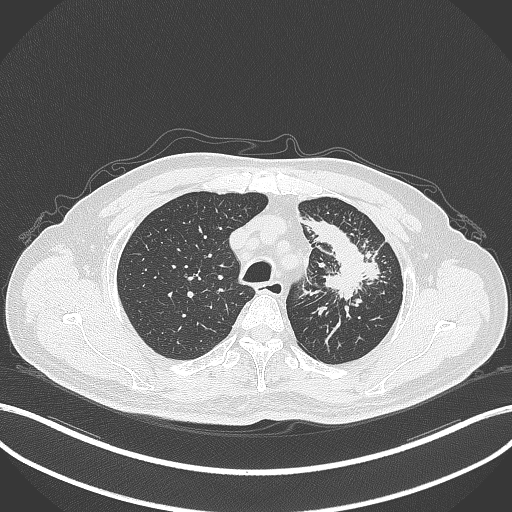
Chest CT, one axial slice; position 280 of 386 along the scan axis; reconstruction kernel B70f; 120 kVp; lung window (W 1500 / L -600 HU); 1 mm slice thickness; 512 × 512 image matrix, field of view 400 × 400 mm. Male patient, age 69 years. Case-level facts recorded for this patient, not image findings: clinical TNM (as recorded): T2a N2 M0.
Structures marked on this image (bounding box drawn by a radiologist):
- lung tumour (recorded histology: adenocarcinoma): bounding box [x1, y1, x2, y2] px = [302, 213, 388, 305]